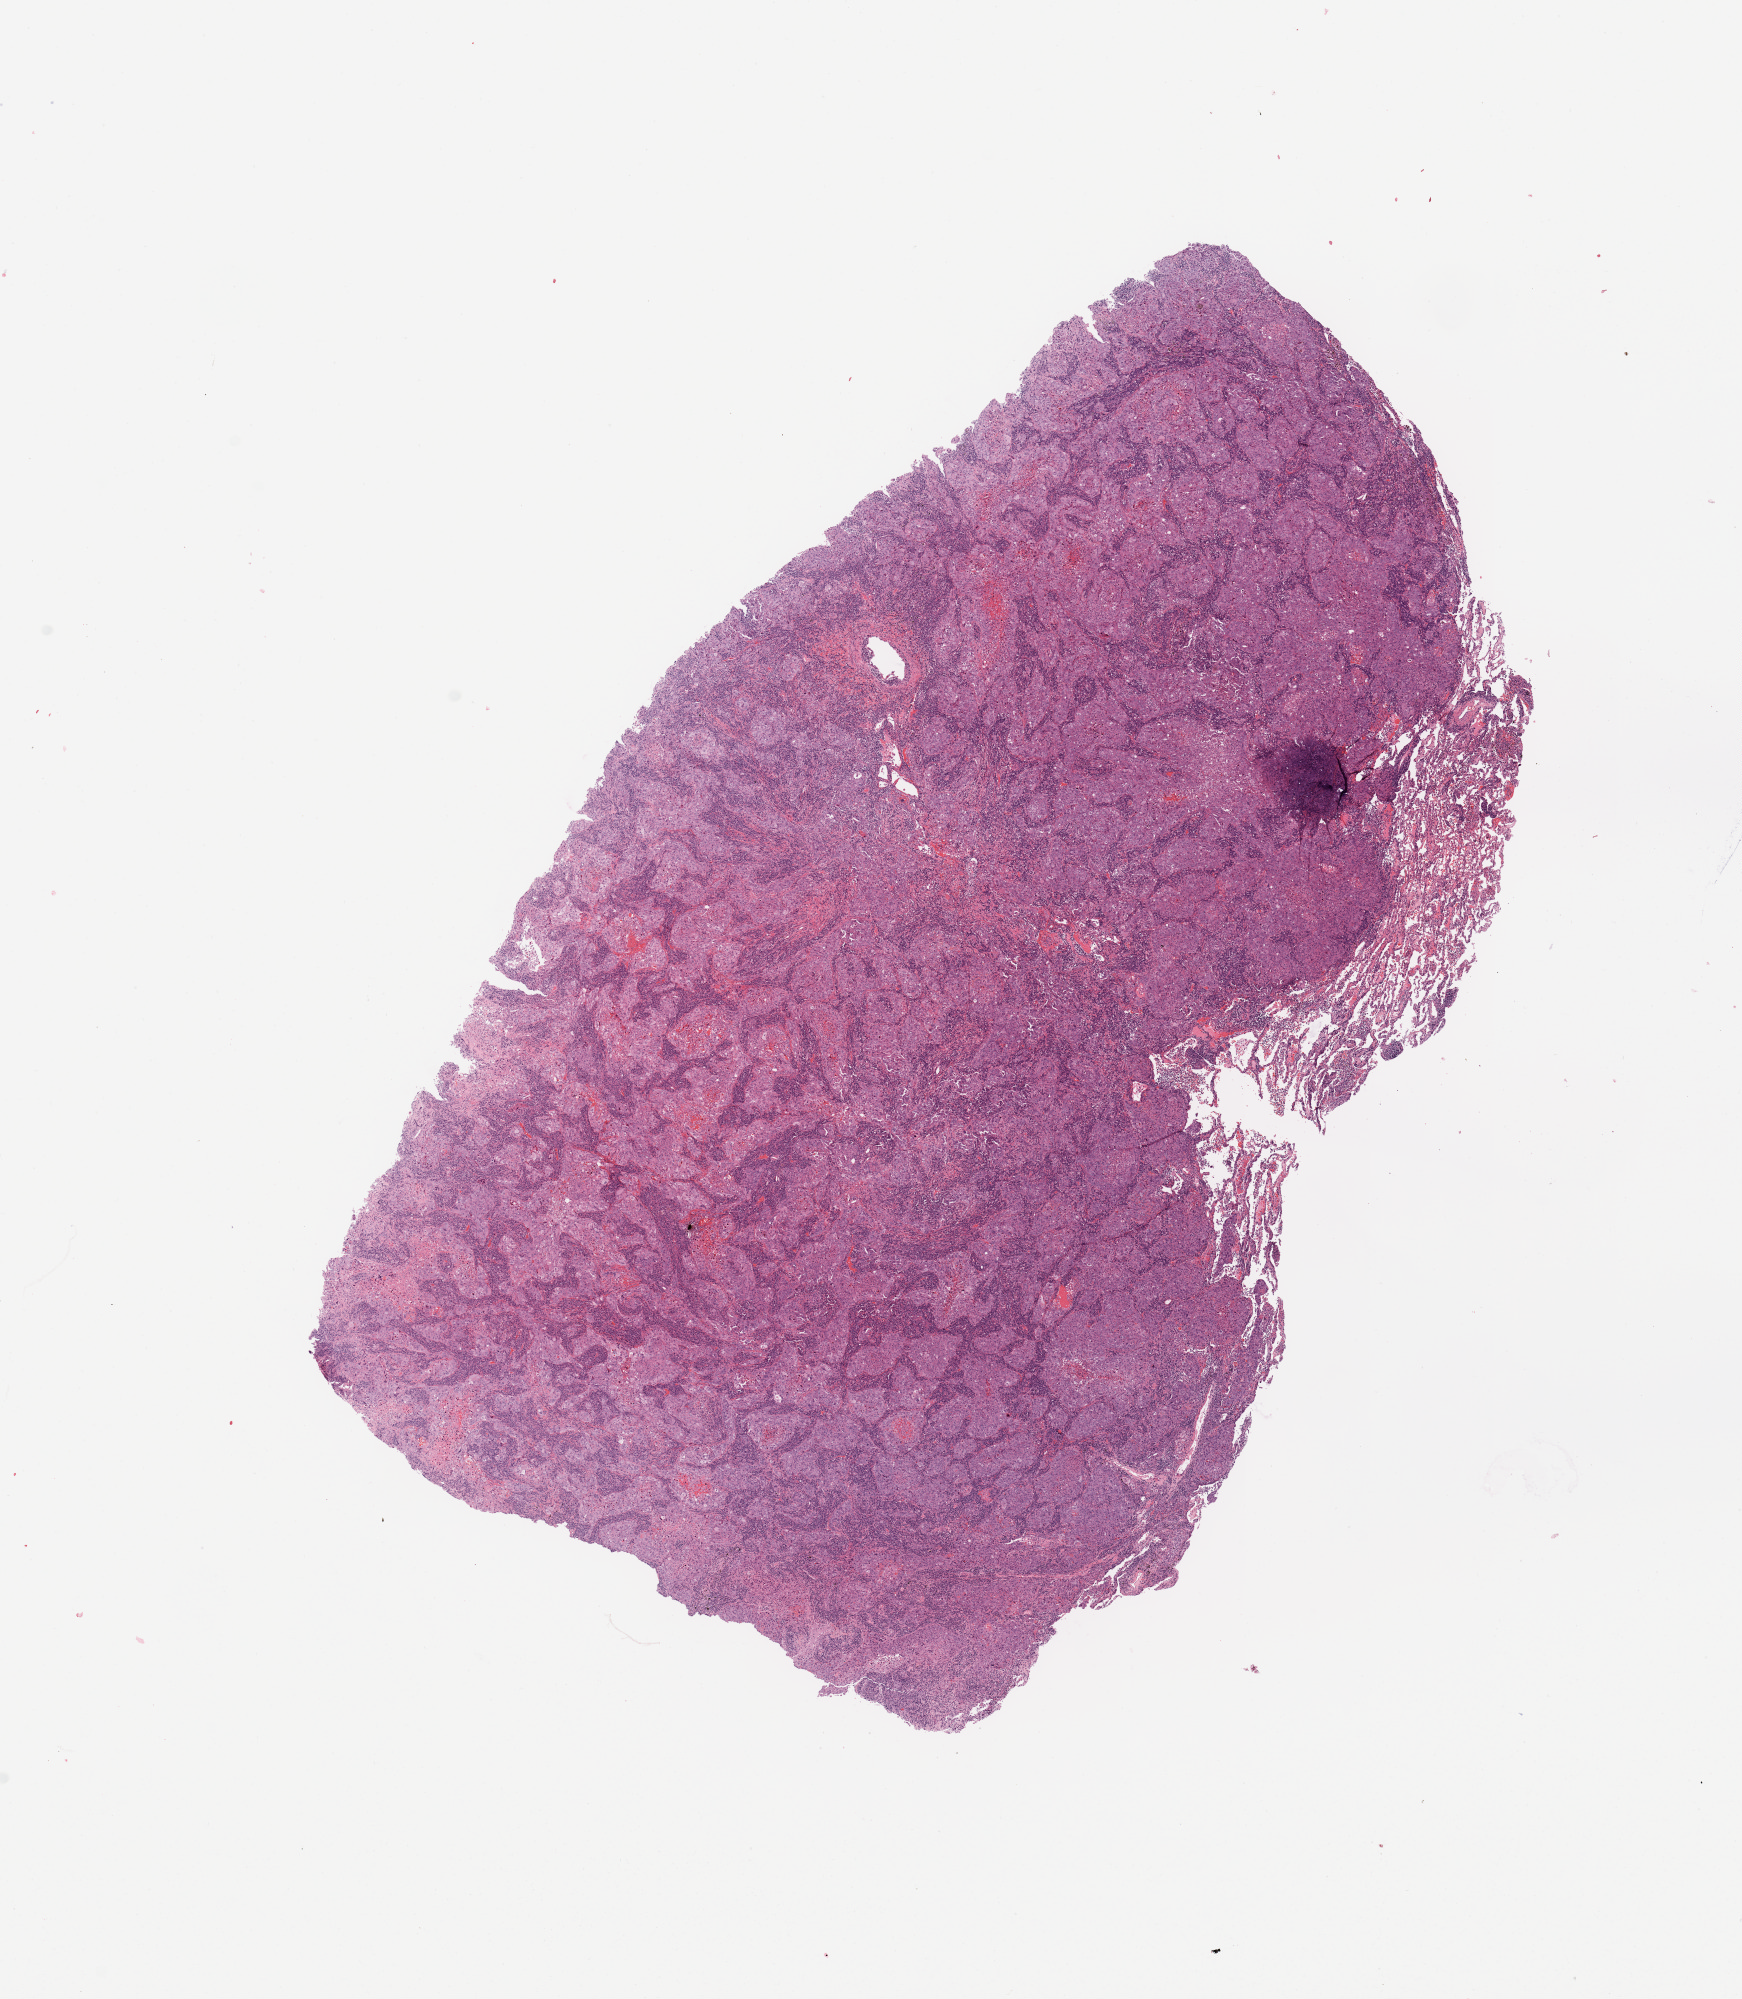
Digitized H&E-stained tissue section (whole slide), whole scanned area (about 13.8 x 15.8 mm) shown as a low-resolution overview, tumour tissue sample, sampled site: lung. Patient: male, age 64 years. Histologic grade: G3 (poorly differentiated). Slide review estimates, as recorded: tumour nuclei 60%, necrosis 2%.
Primary tumour site (as recorded): left upper lobe. Diagnosis: Adenocarcinoma, NOS. AJCC pathologic stage: IIIA.